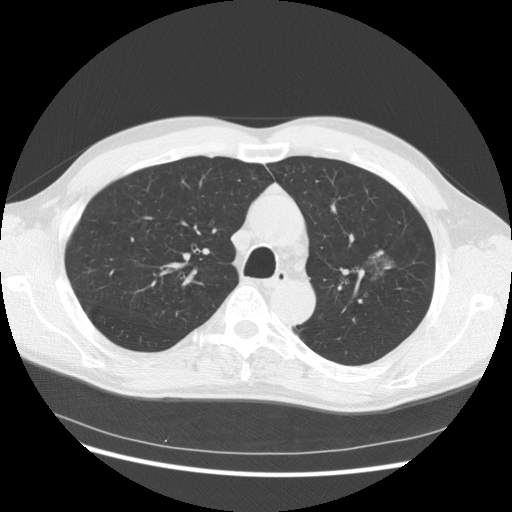
Chest CT (low-dose screening protocol), one axial image; third screening round (two years after baseline); lung window (W 1500 / L -600 HU); 2.5 mm slice thickness; standard (soft-tissue) reconstruction kernel (STANDARD); slice 98 of 145 in the series; 512 × 512 image matrix. Male participant, aged 61 years at enrolment.
• Expert-annotated lung lesion, bounding box <332,223,416,305> (left, top, right, bottom; pixels).
• Screening reader's record for this exam (one nodule recorded; not confirmed to be the boxed lesion): non-calcified nodule or mass ≥4 mm, left upper lobe, 37 × 33 mm, poorly defined margins, mixed attenuation, pre-existing on the prior screen: yes; interval growth: yes.
• Lung cancer was diagnosed 361 days after this screen: bronchiolo-alveolar adenocarcinoma, NOS, left upper lobe, well differentiated (G1), stage IB (AJCC 6th edition), 44 mm at pathology.